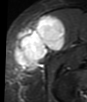
MRI of an extremity soft-tissue mass, one axial slice; STIR; MR volume resampled by the dataset authors to the PET/CT grid (not the native acquisition matrix); 87 × 102 image matrix. Female patient. From the clinical record (not read from this slice): histological type: synovial sarcoma; grade: intermediate; site of the primary tumour: right thigh.
Annotated regions visible in this slice (expert contour drawn on MRI and transferred to this co-registered scan by the dataset authors):
- gross tumour volume including surrounding oedema: box from (x=15, y=15) to (x=66, y=71) px
- gross tumour volume (mass): (x=15, y=15)–(x=66, y=71)